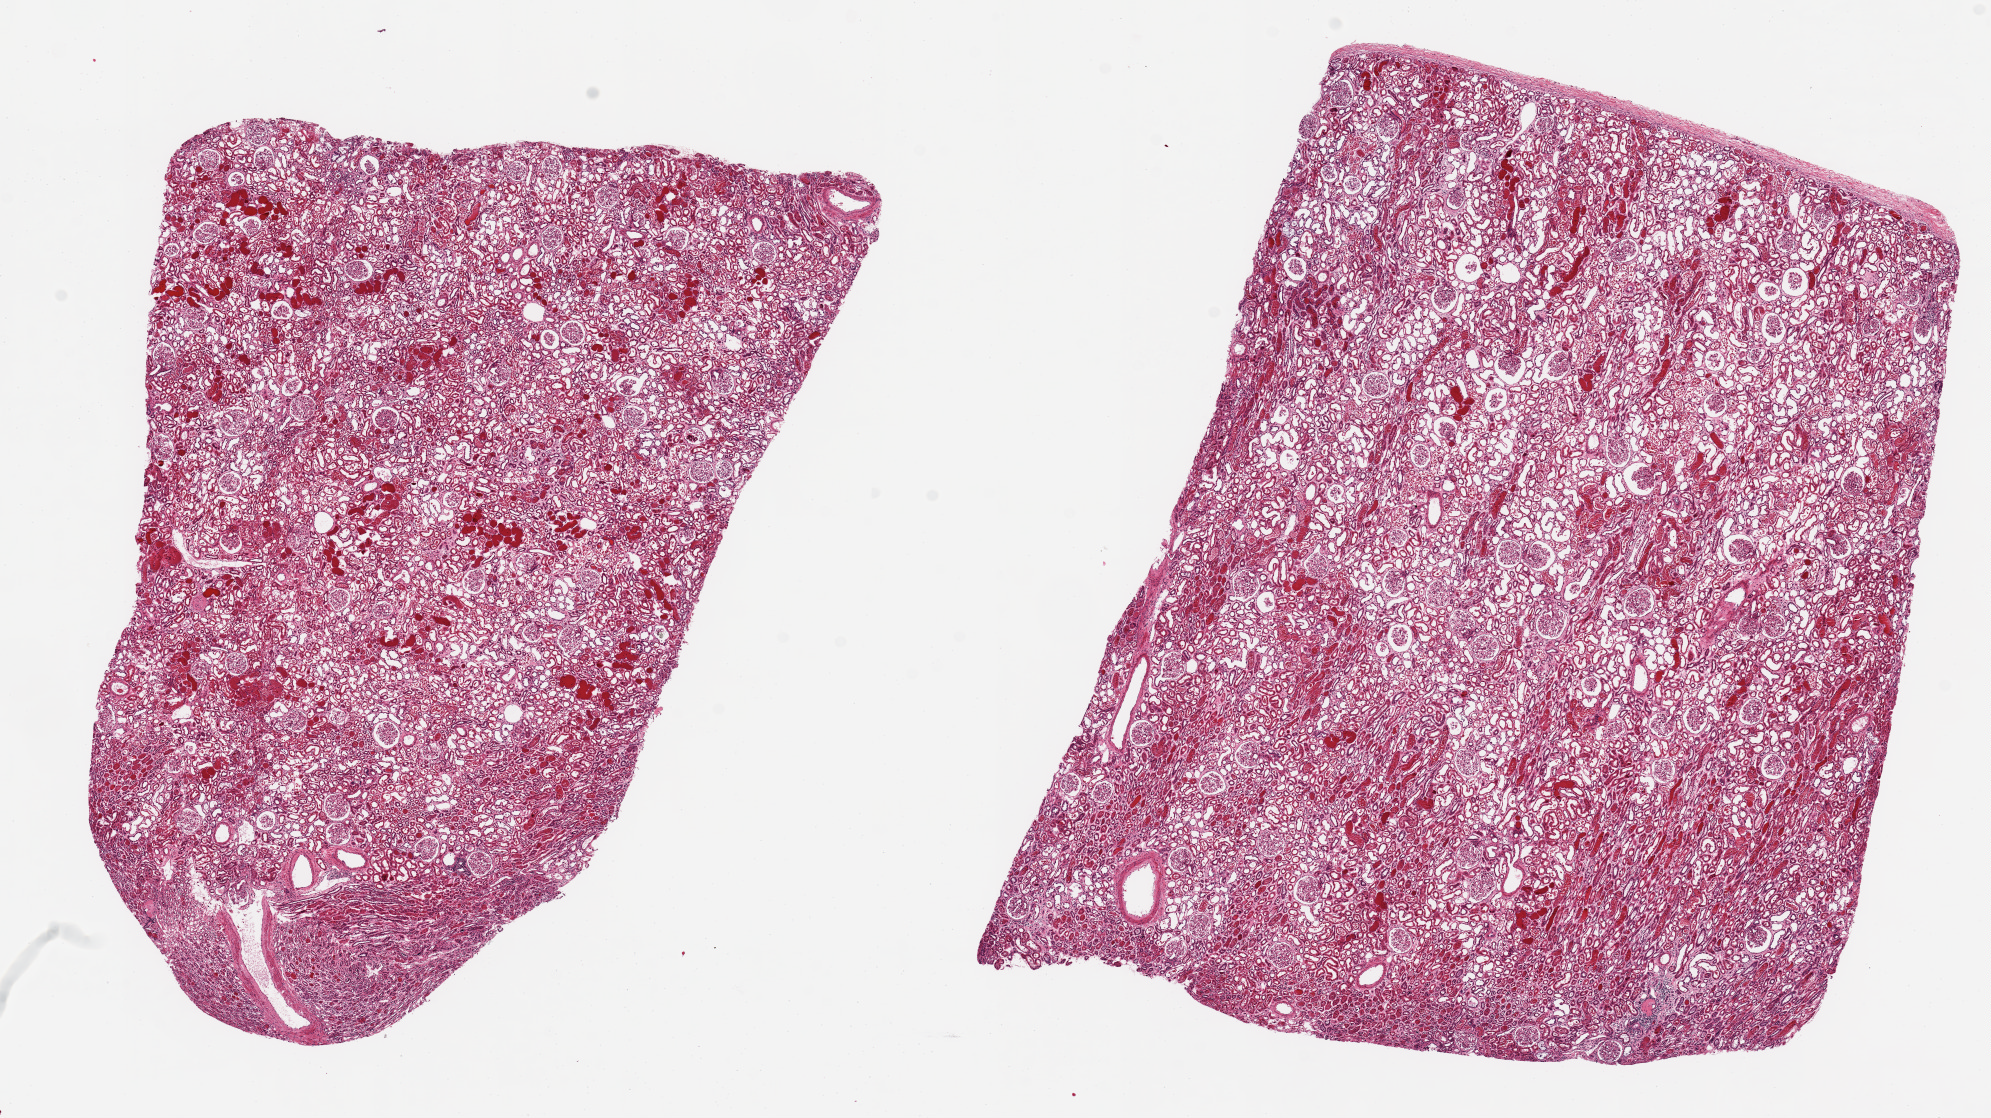
Whole-slide image, H&E stain, brightfield, a low-resolution overview of the entire scanned area, about 15.8 x 8.8 mm, PAXgene-fixed paraffin-embedded (PFPE) section, sampled site (target tissue): renal cortex, donor tissue sample. Donor: male.
• review note (as recorded): 2 pieces ~7.5x6 mm; cortex, not medulla, except for 10% of 1 piece; numerous red cell casts